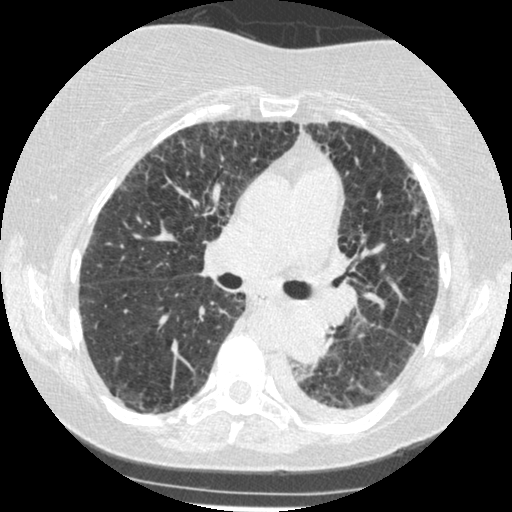
Low-dose screening chest CT, axial slice. Third annual screen. Lung window (W 1500 / L -600 HU). Standard (soft-tissue) reconstruction kernel (STANDARD). Slice 189 of 341 in the series. Female, age 60 years at enrolment. Former smoker at enrolment.
Expert-annotated lung lesion, bounding box [x1, y1, x2, y2] px = [269, 308, 341, 373]. Reader record for this screening exam (exam-level; its link to the box is not recorded): non-calcified nodule or mass ≥4 mm, left lower lobe, 54 × 38 mm, smooth margins, soft tissue attenuation, pre-existing on the prior screen: yes; interval growth: yes. Later outcome: lung cancer diagnosed 15 days after this screen — small cell carcinoma, NOS, left lower lobe, undifferentiated (G4), stage IV (AJCC 6th edition), 69 mm at pathology.